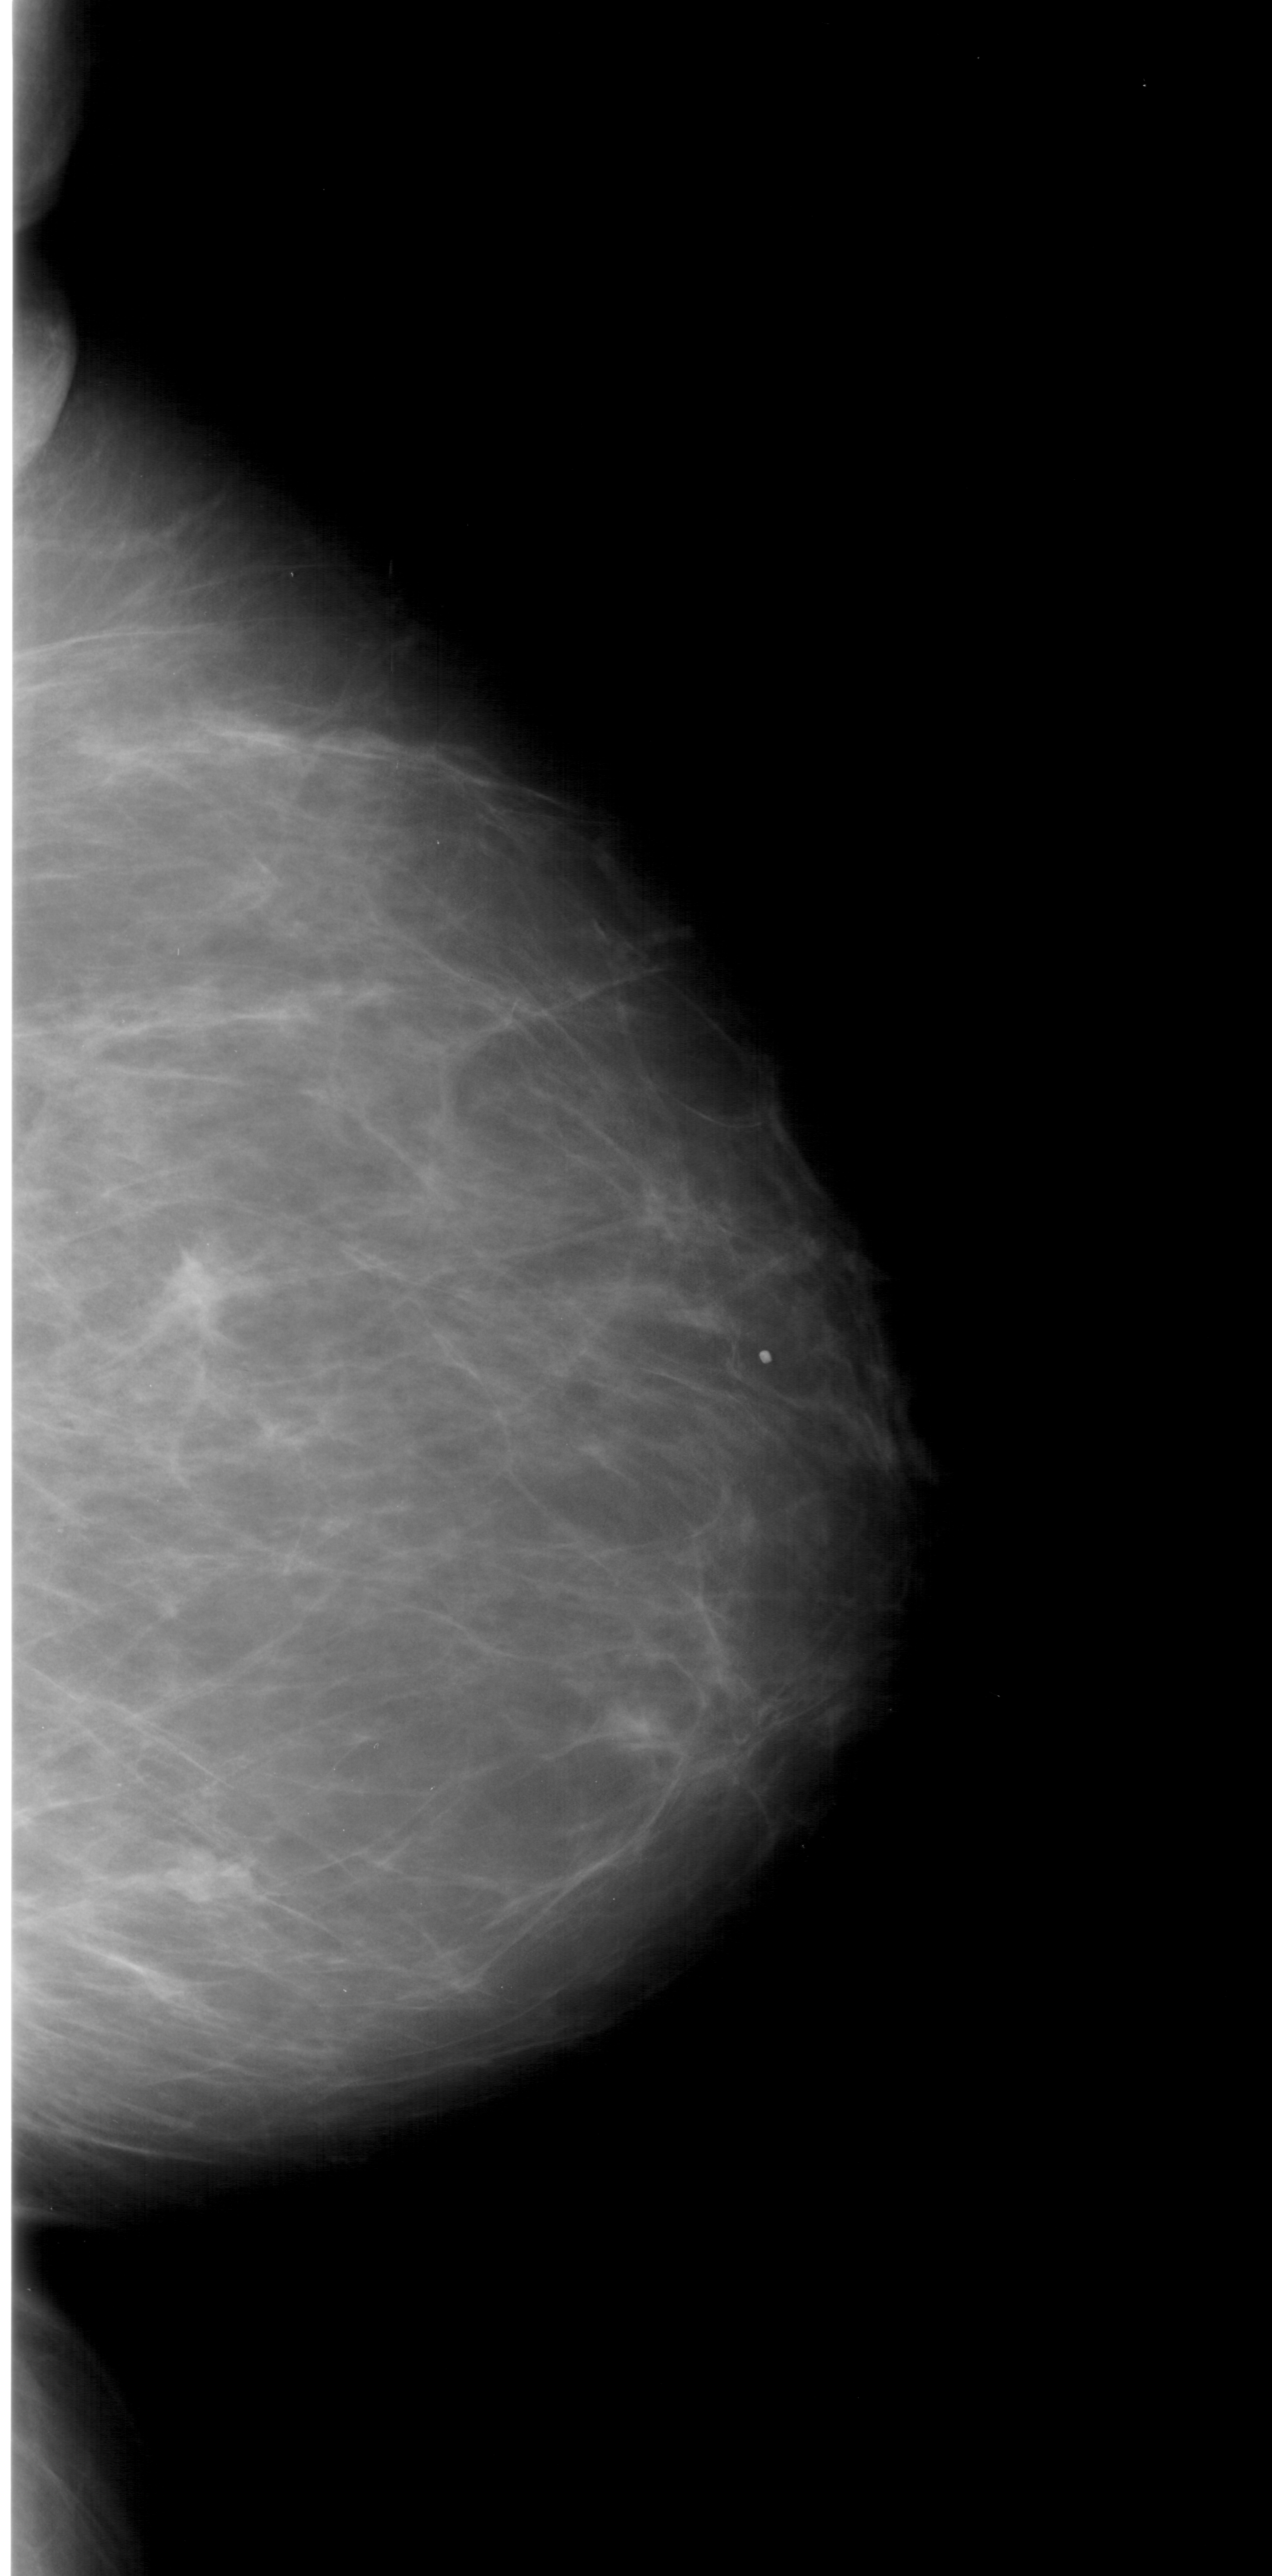
Digitized screen-film mammogram; right breast; craniocaudal (CC) view; BI-RADS breast density category 3 (scale 1–4).
- Mass, shape irregular, margins spiculated; BI-RADS assessment category 5; pathology (as recorded): malignant.